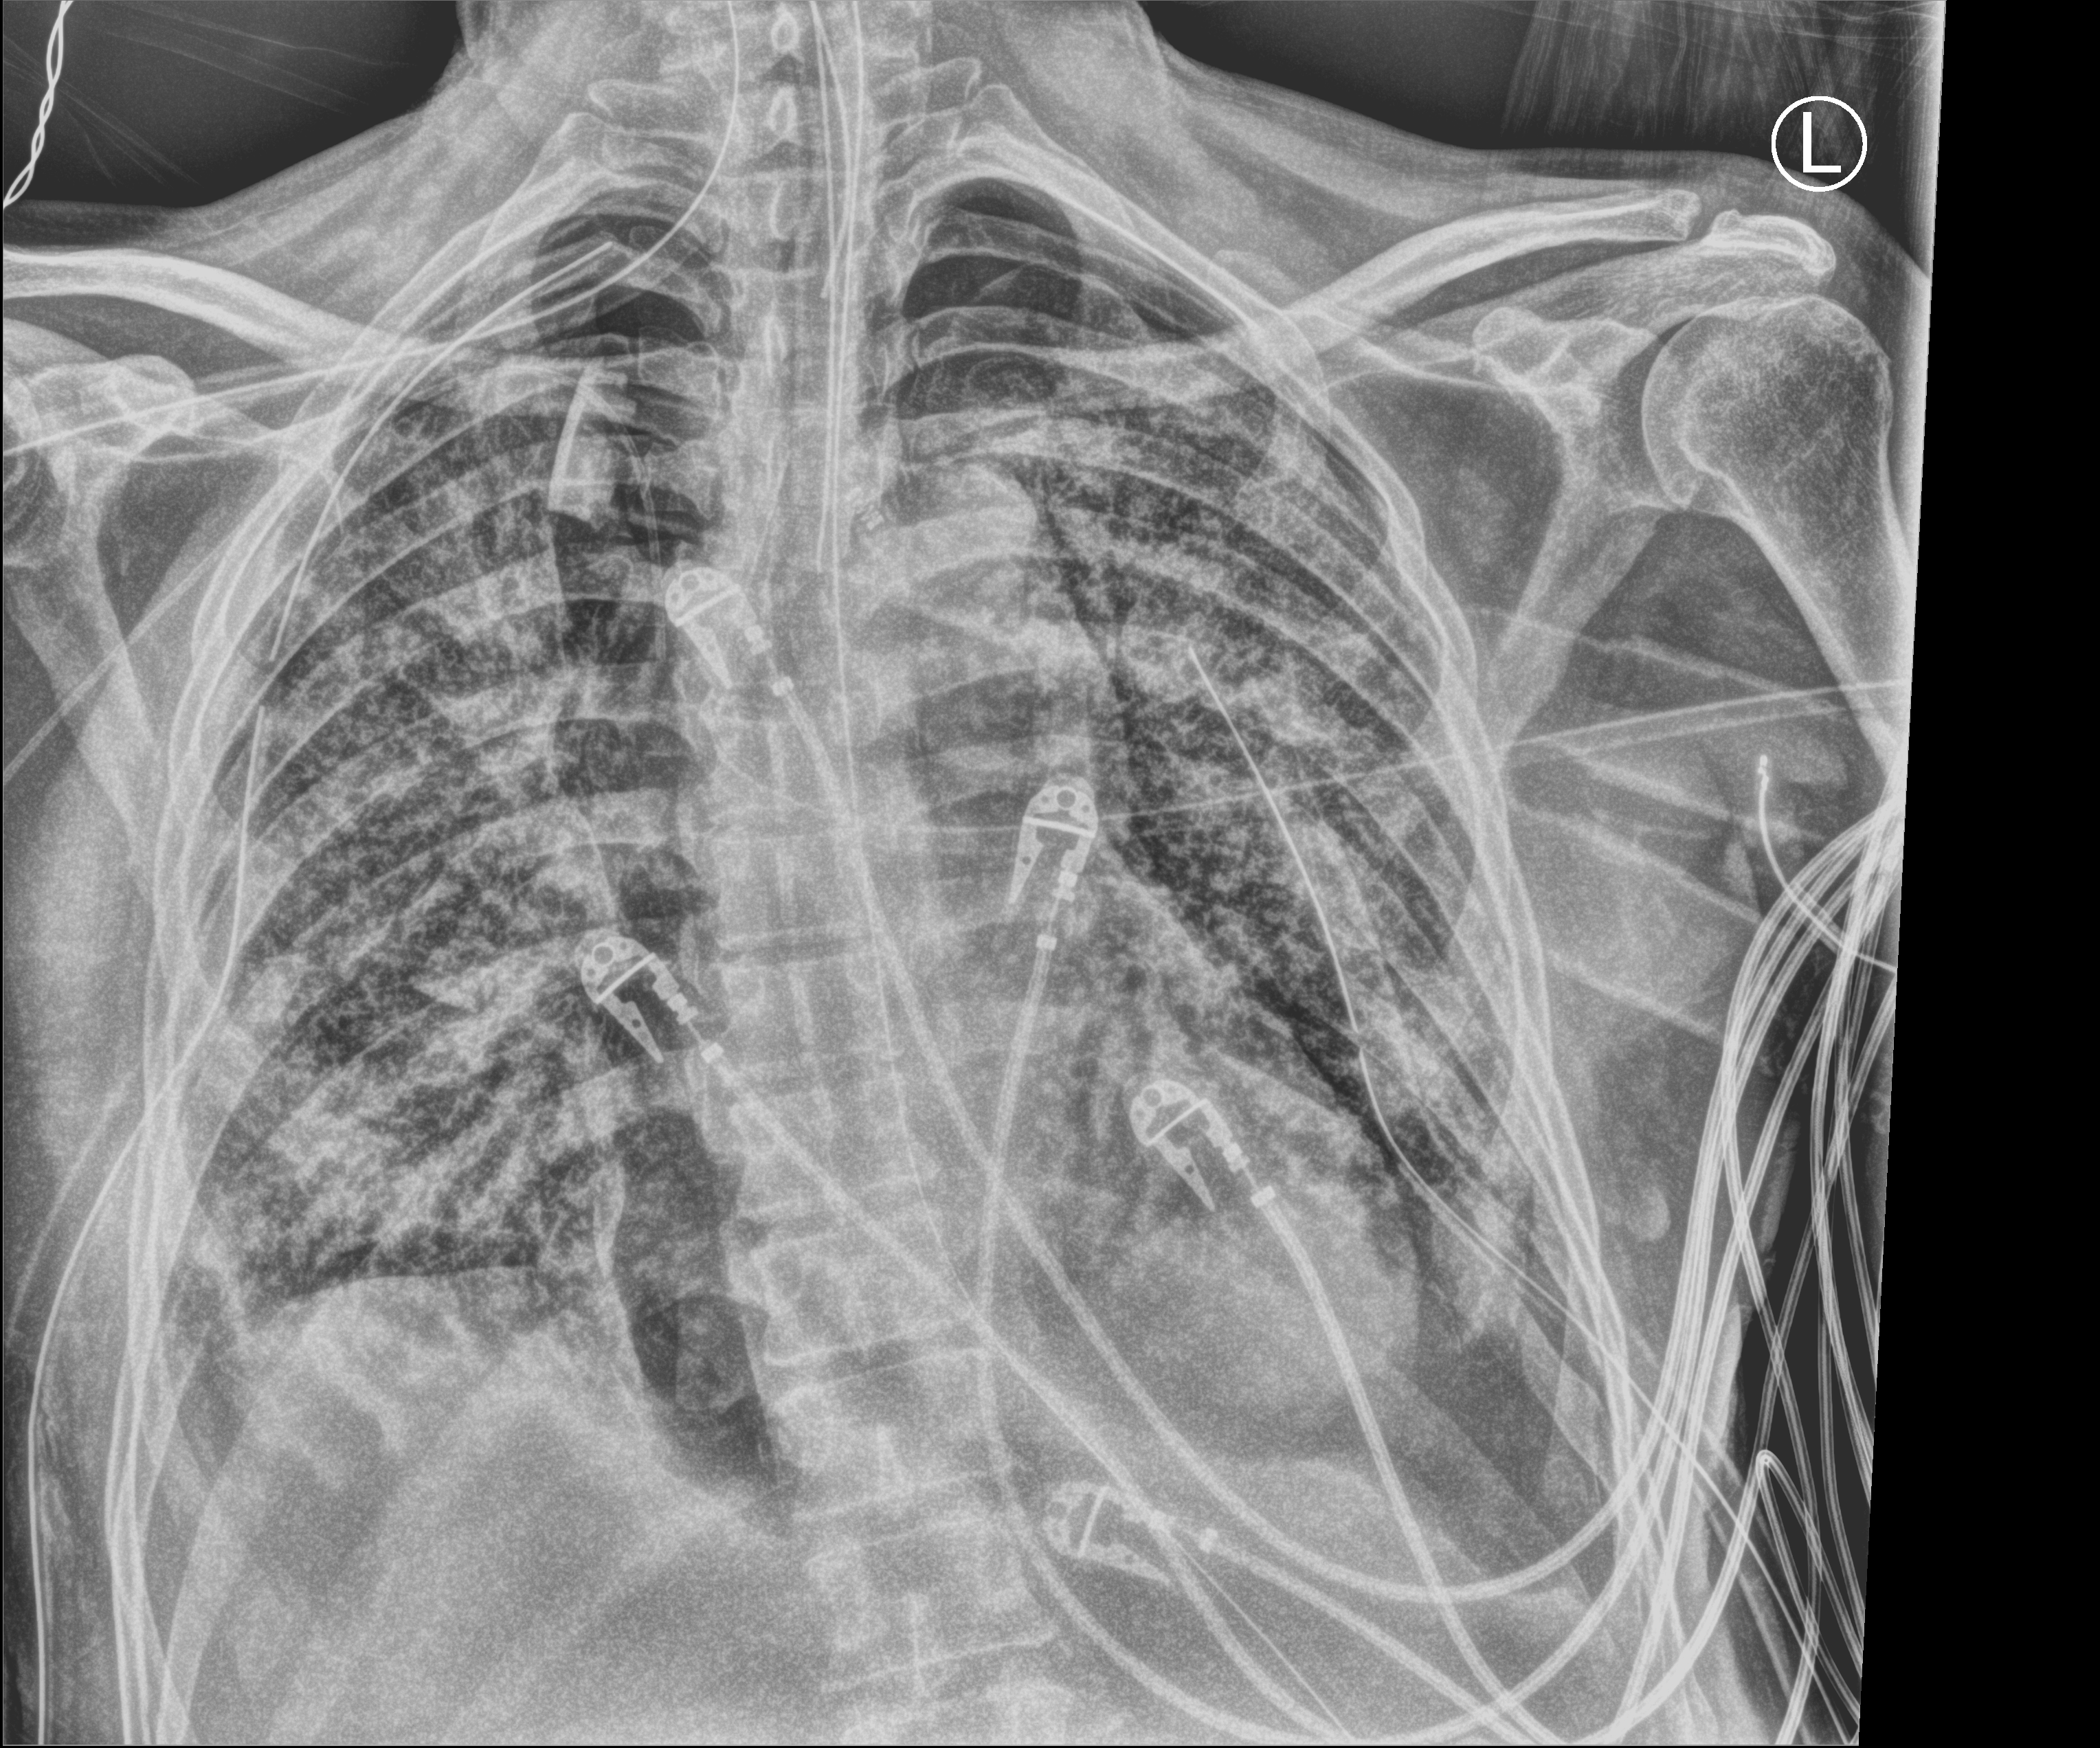
Chest X-ray (portable), anteroposterior (AP) projection. Male patient hospitalised with COVID-19, age 60–74 years.
Admission-level facts for this patient (not findings on this image; timing relative to this image not recorded):
- admitted to intensive care during this hospital stay: yes